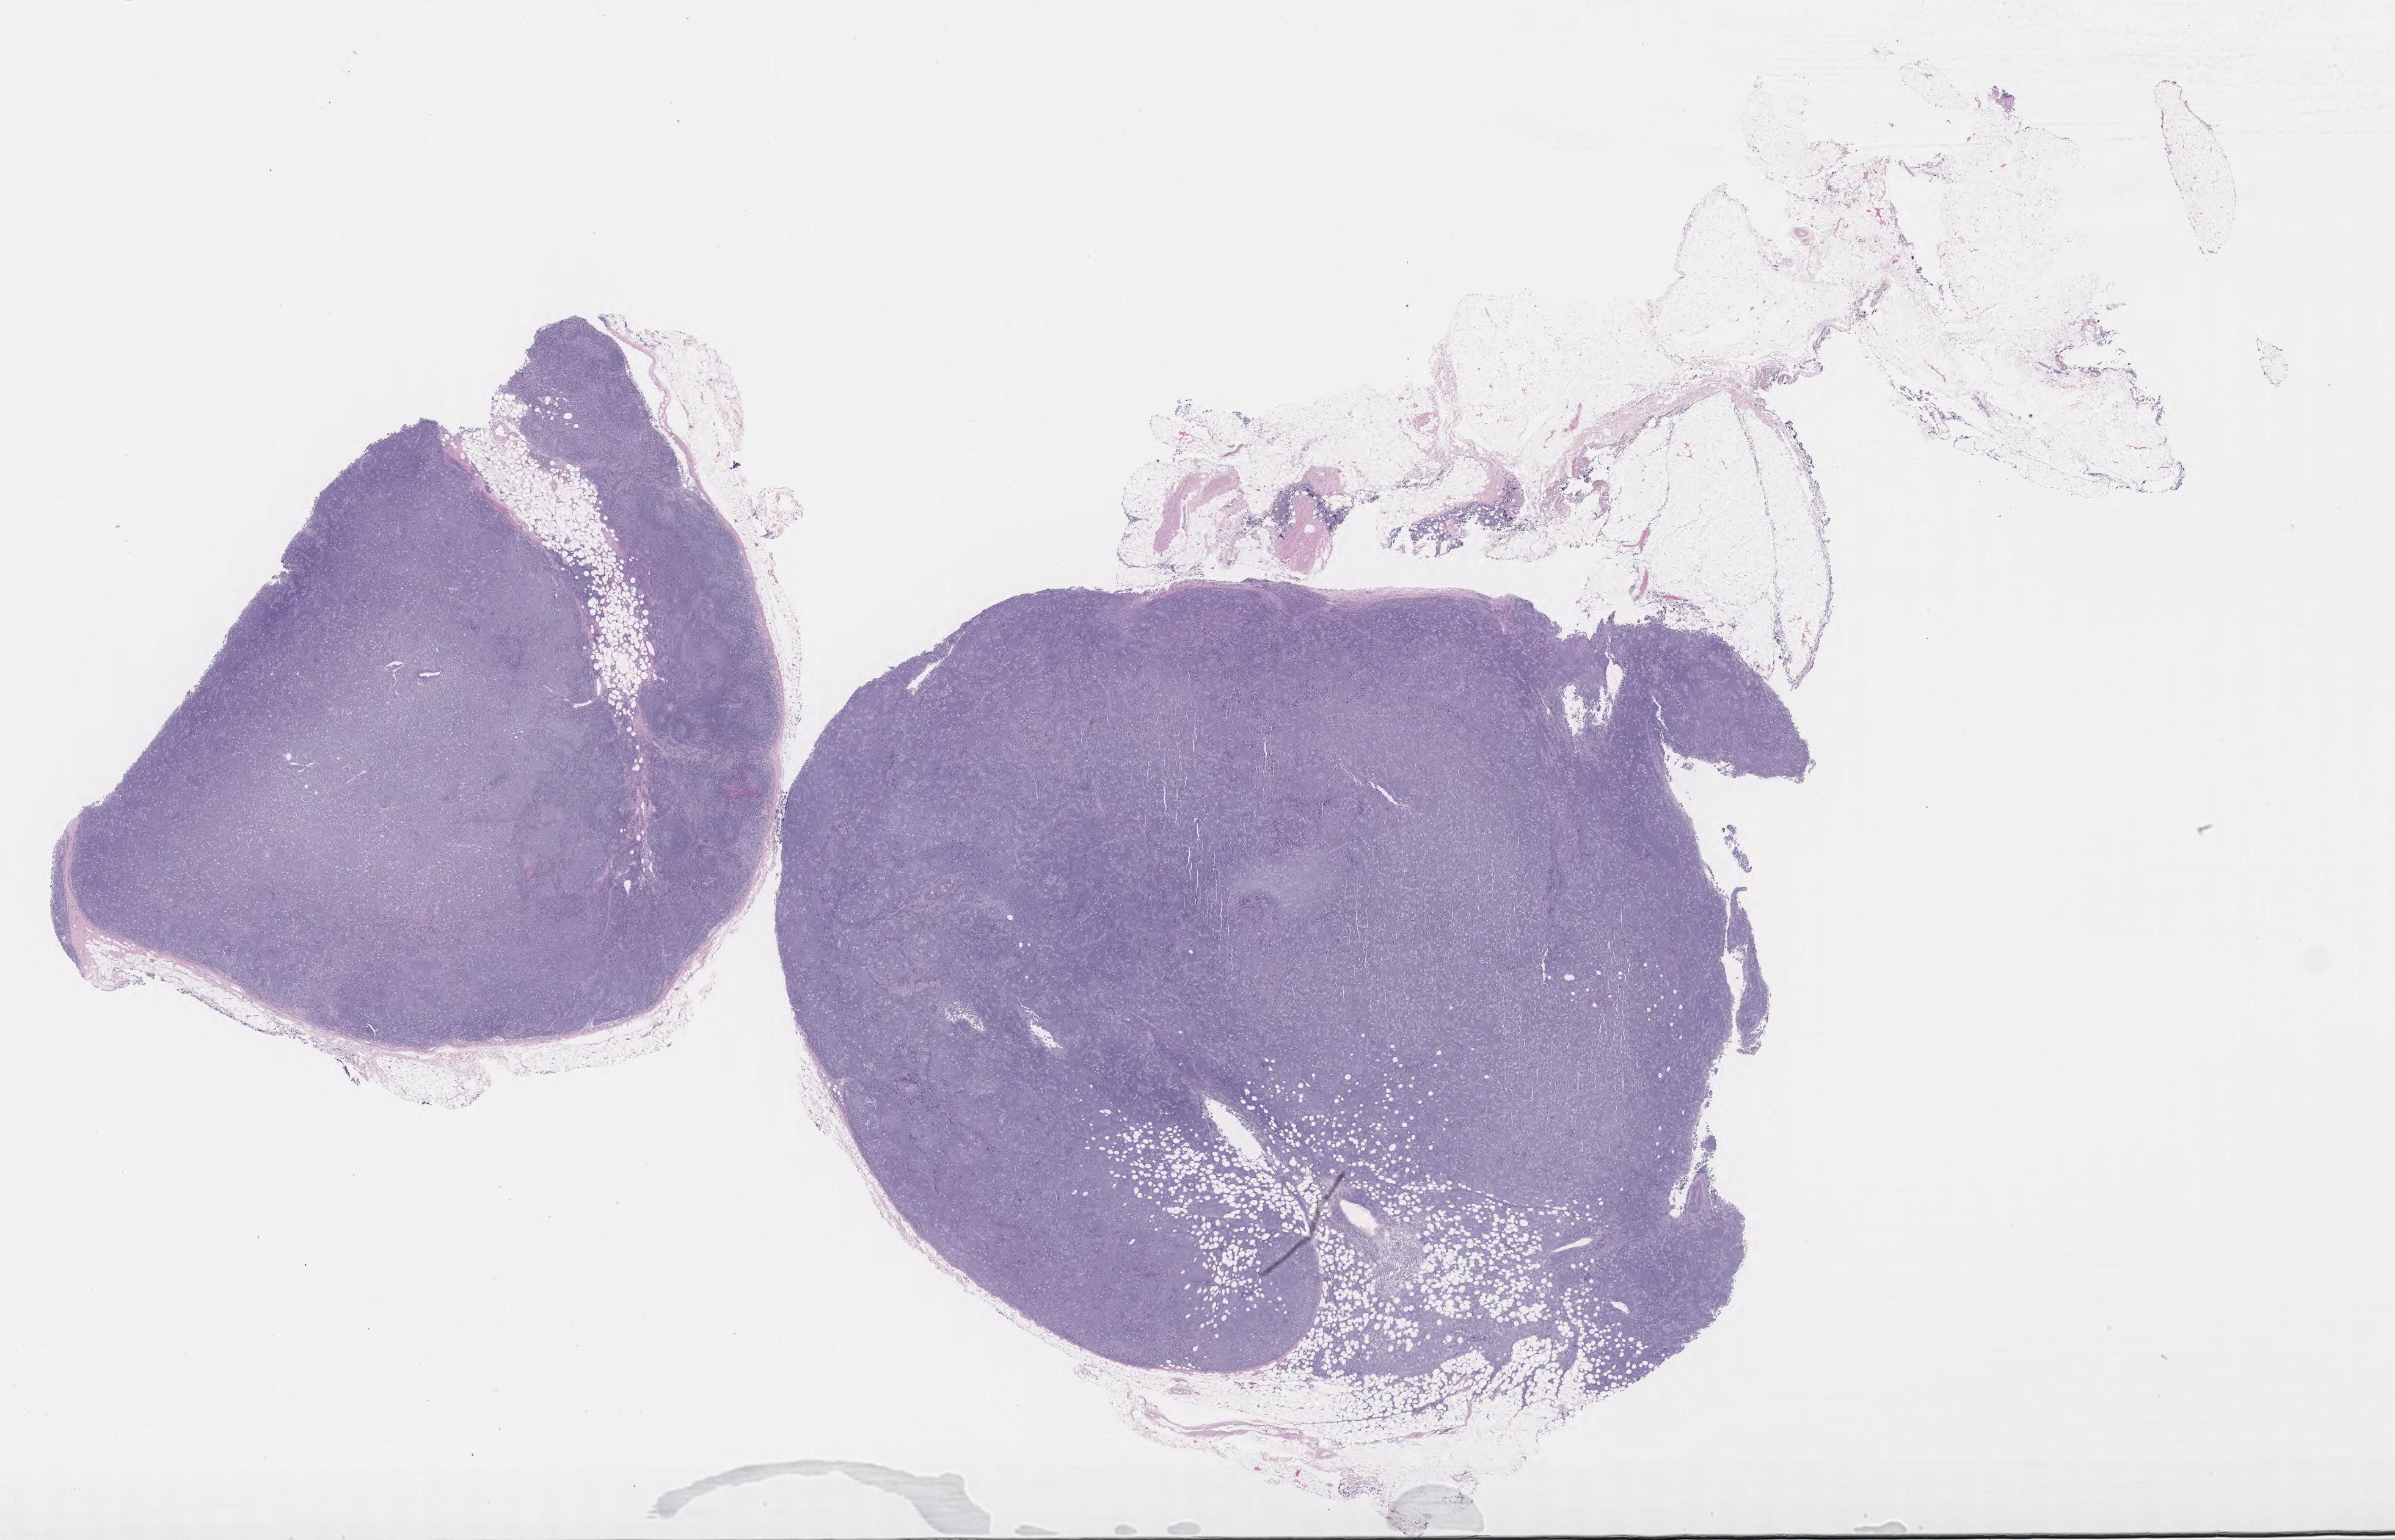
Digitized H&E-stained section, a low-resolution overview of the entire scanned area, about 31.7 x 20.4 mm. Tumor tissue. Anatomic site: upper limb lymph node. Patient: male, aged 71.
• diagnosis: Burkitt lymphoma, NOS